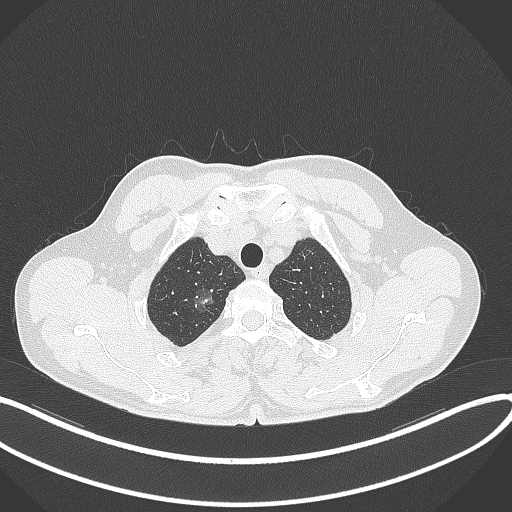
Chest CT, one axial slice; position 334 of 407 along the scan axis; reconstruction kernel B70f; lung window (W 1500 / L -600 HU); 1 mm slice thickness; 512 × 512 image matrix. Patient: male, 58 years. From the clinical record (not read from this slice): clinical TNM (as recorded): T1c N0 M0.
Outlined on this slice (rectangle marked by the reading radiologist):
- lung tumour (recorded histology: adenocarcinoma): bounding box <187,281,226,318> (left, top, right, bottom; pixels)